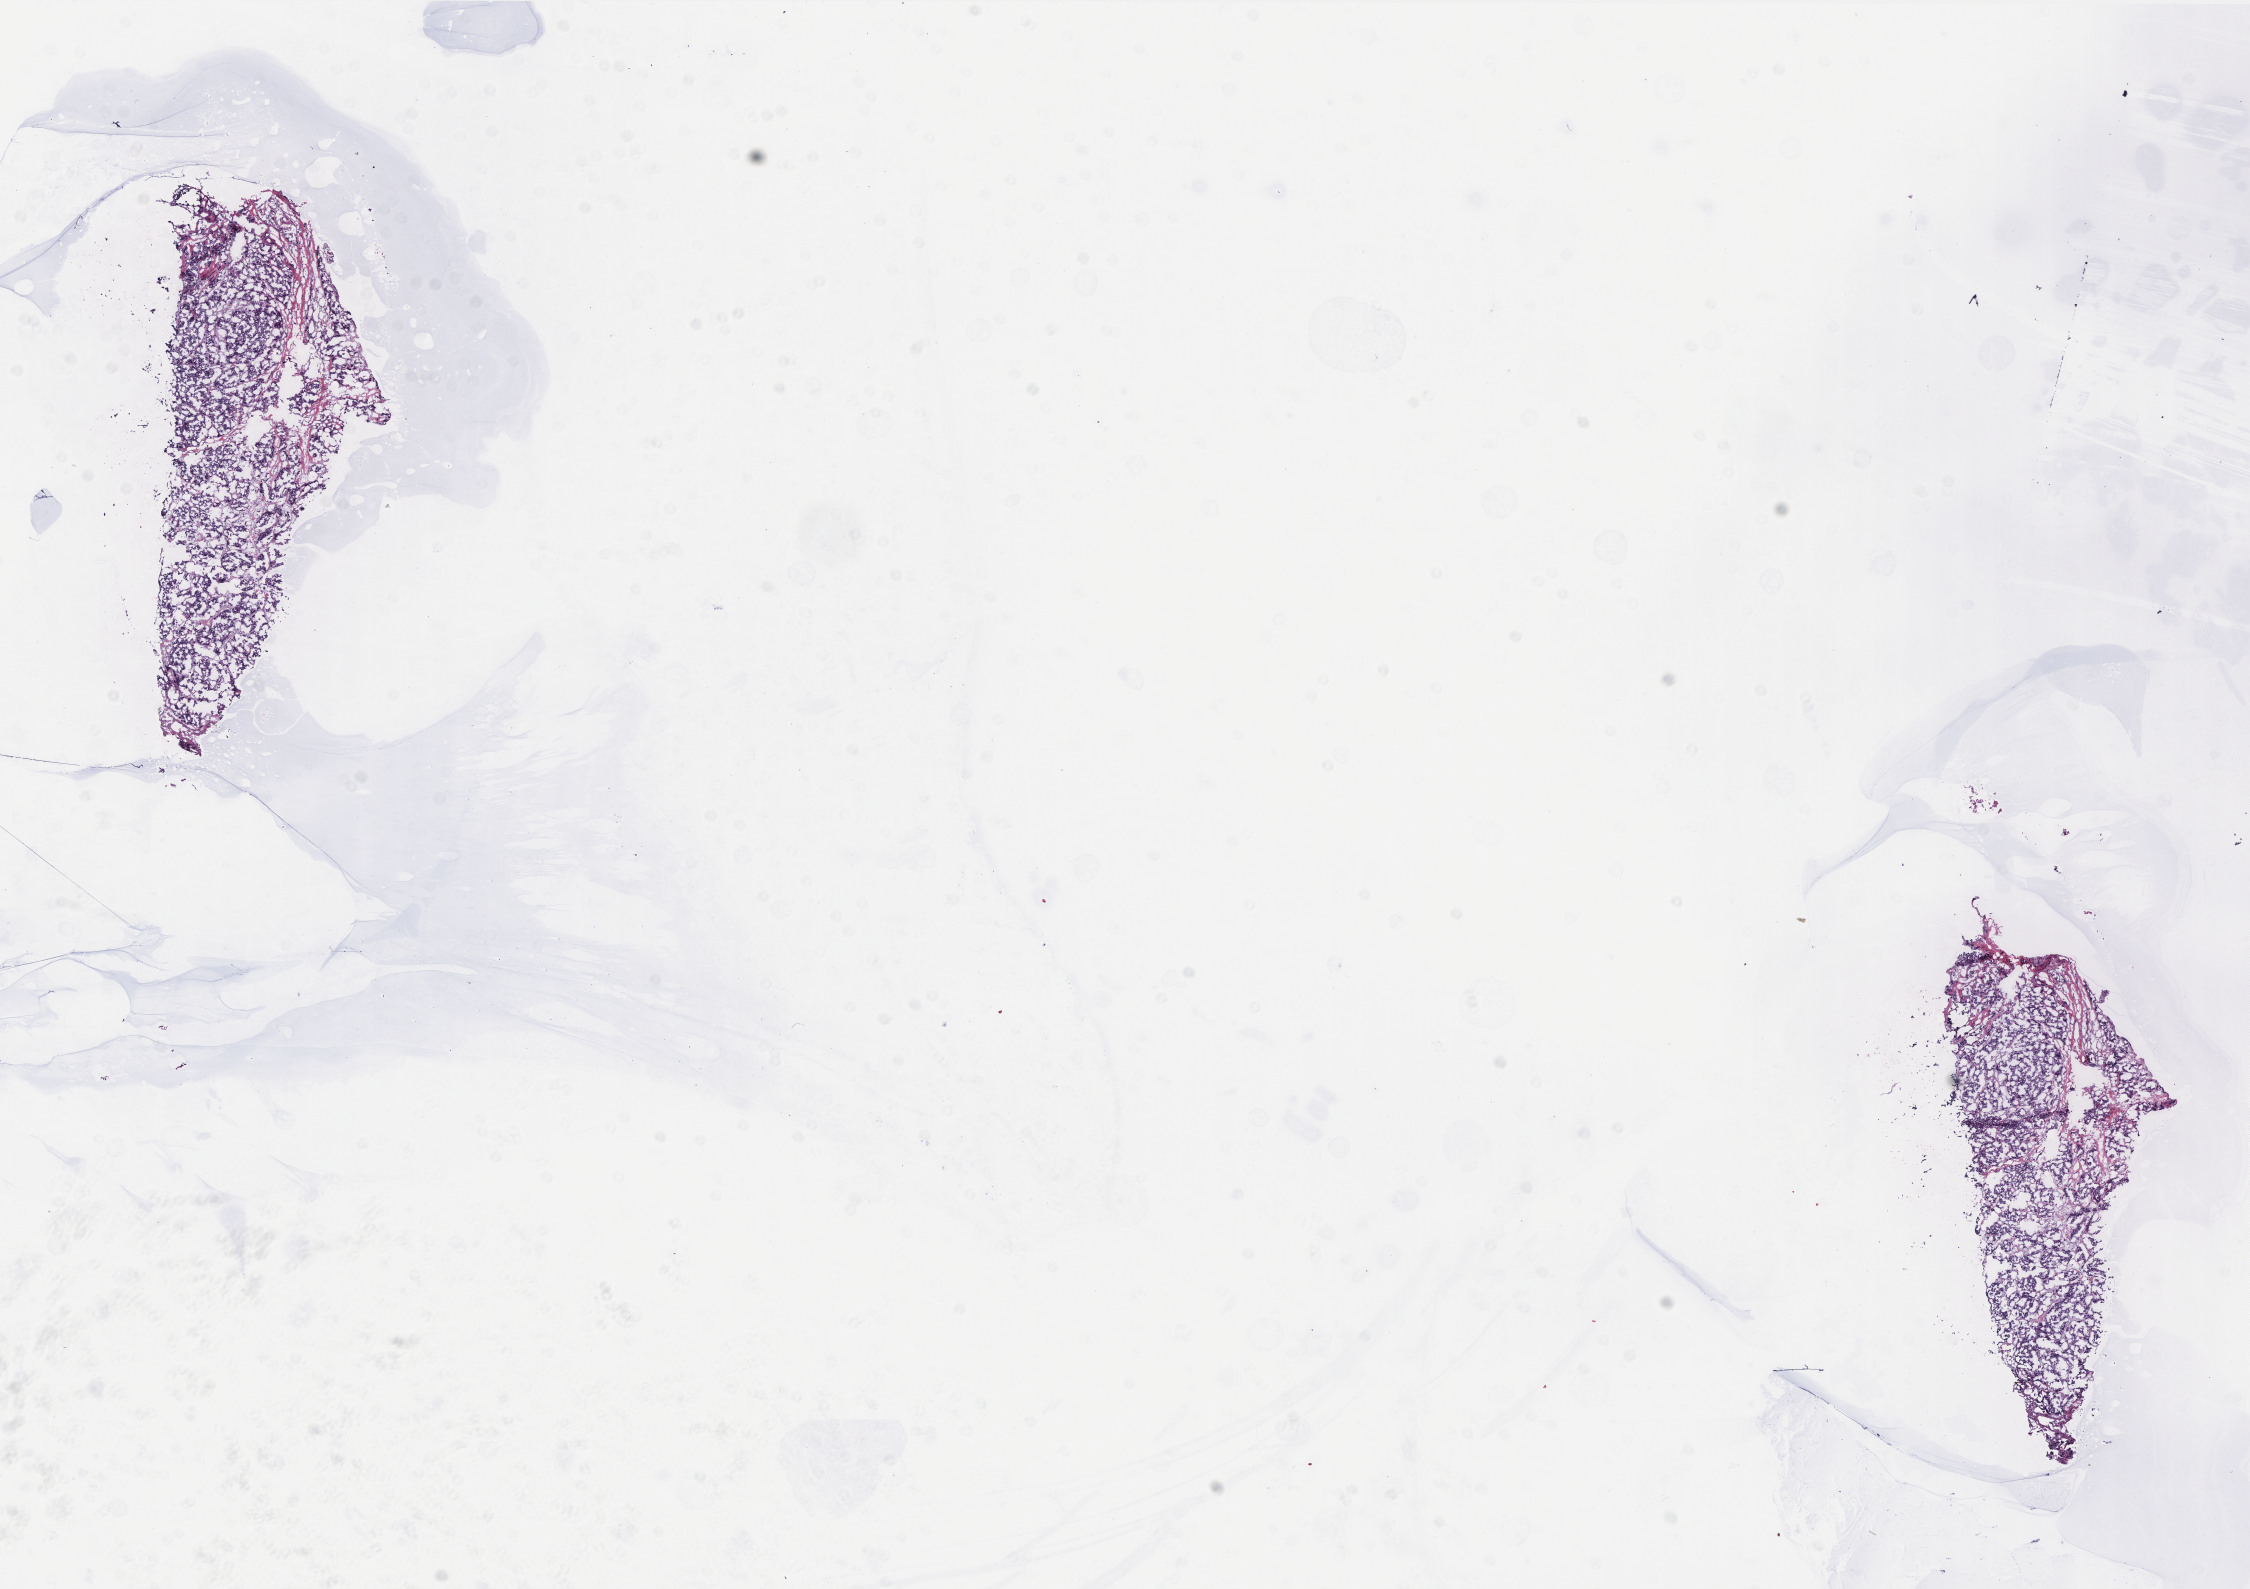
Digitized H&E-stained tissue section (whole slide) — shown as a low-resolution overview of the whole scanned area (about 18.0 x 12.7 mm); frozen section; breast, primary tumour sample. Patient: female, age at initial diagnosis 42 years. Pathologist review of this section (percent, as recorded): tumour cells 80%, tumour nuclei 90%, normal cells 0%, stromal cells 19%, necrosis 1%. Infiltration values recorded for this section: lymphocyte infiltration 0%, monocyte infiltration 0%, neutrophil infiltration 0%.
AJCC pathologic stage: IIB (6th edition). Lymph nodes positive (case pathology): 2 of 12 examined. Pathologic diagnosis: Infiltrating duct carcinoma, NOS.